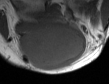
MRI of an extremity soft-tissue mass, one axial slice. Position 20 of 50 along the scan axis. MR volume resampled by the dataset authors to the PET/CT grid (not the native acquisition matrix). 109 × 84 image matrix, field of view 106 × 82 mm. Male patient. Case-level facts recorded for this patient, not image findings: histological type: synovial sarcoma; site of the primary tumour: left poplietal fossa.
Outlined on this slice (expert contour drawn on MRI and transferred to this co-registered scan by the dataset authors):
- gross tumour volume (mass): bounding box [x1, y1, x2, y2] px = [18, 25, 88, 70]